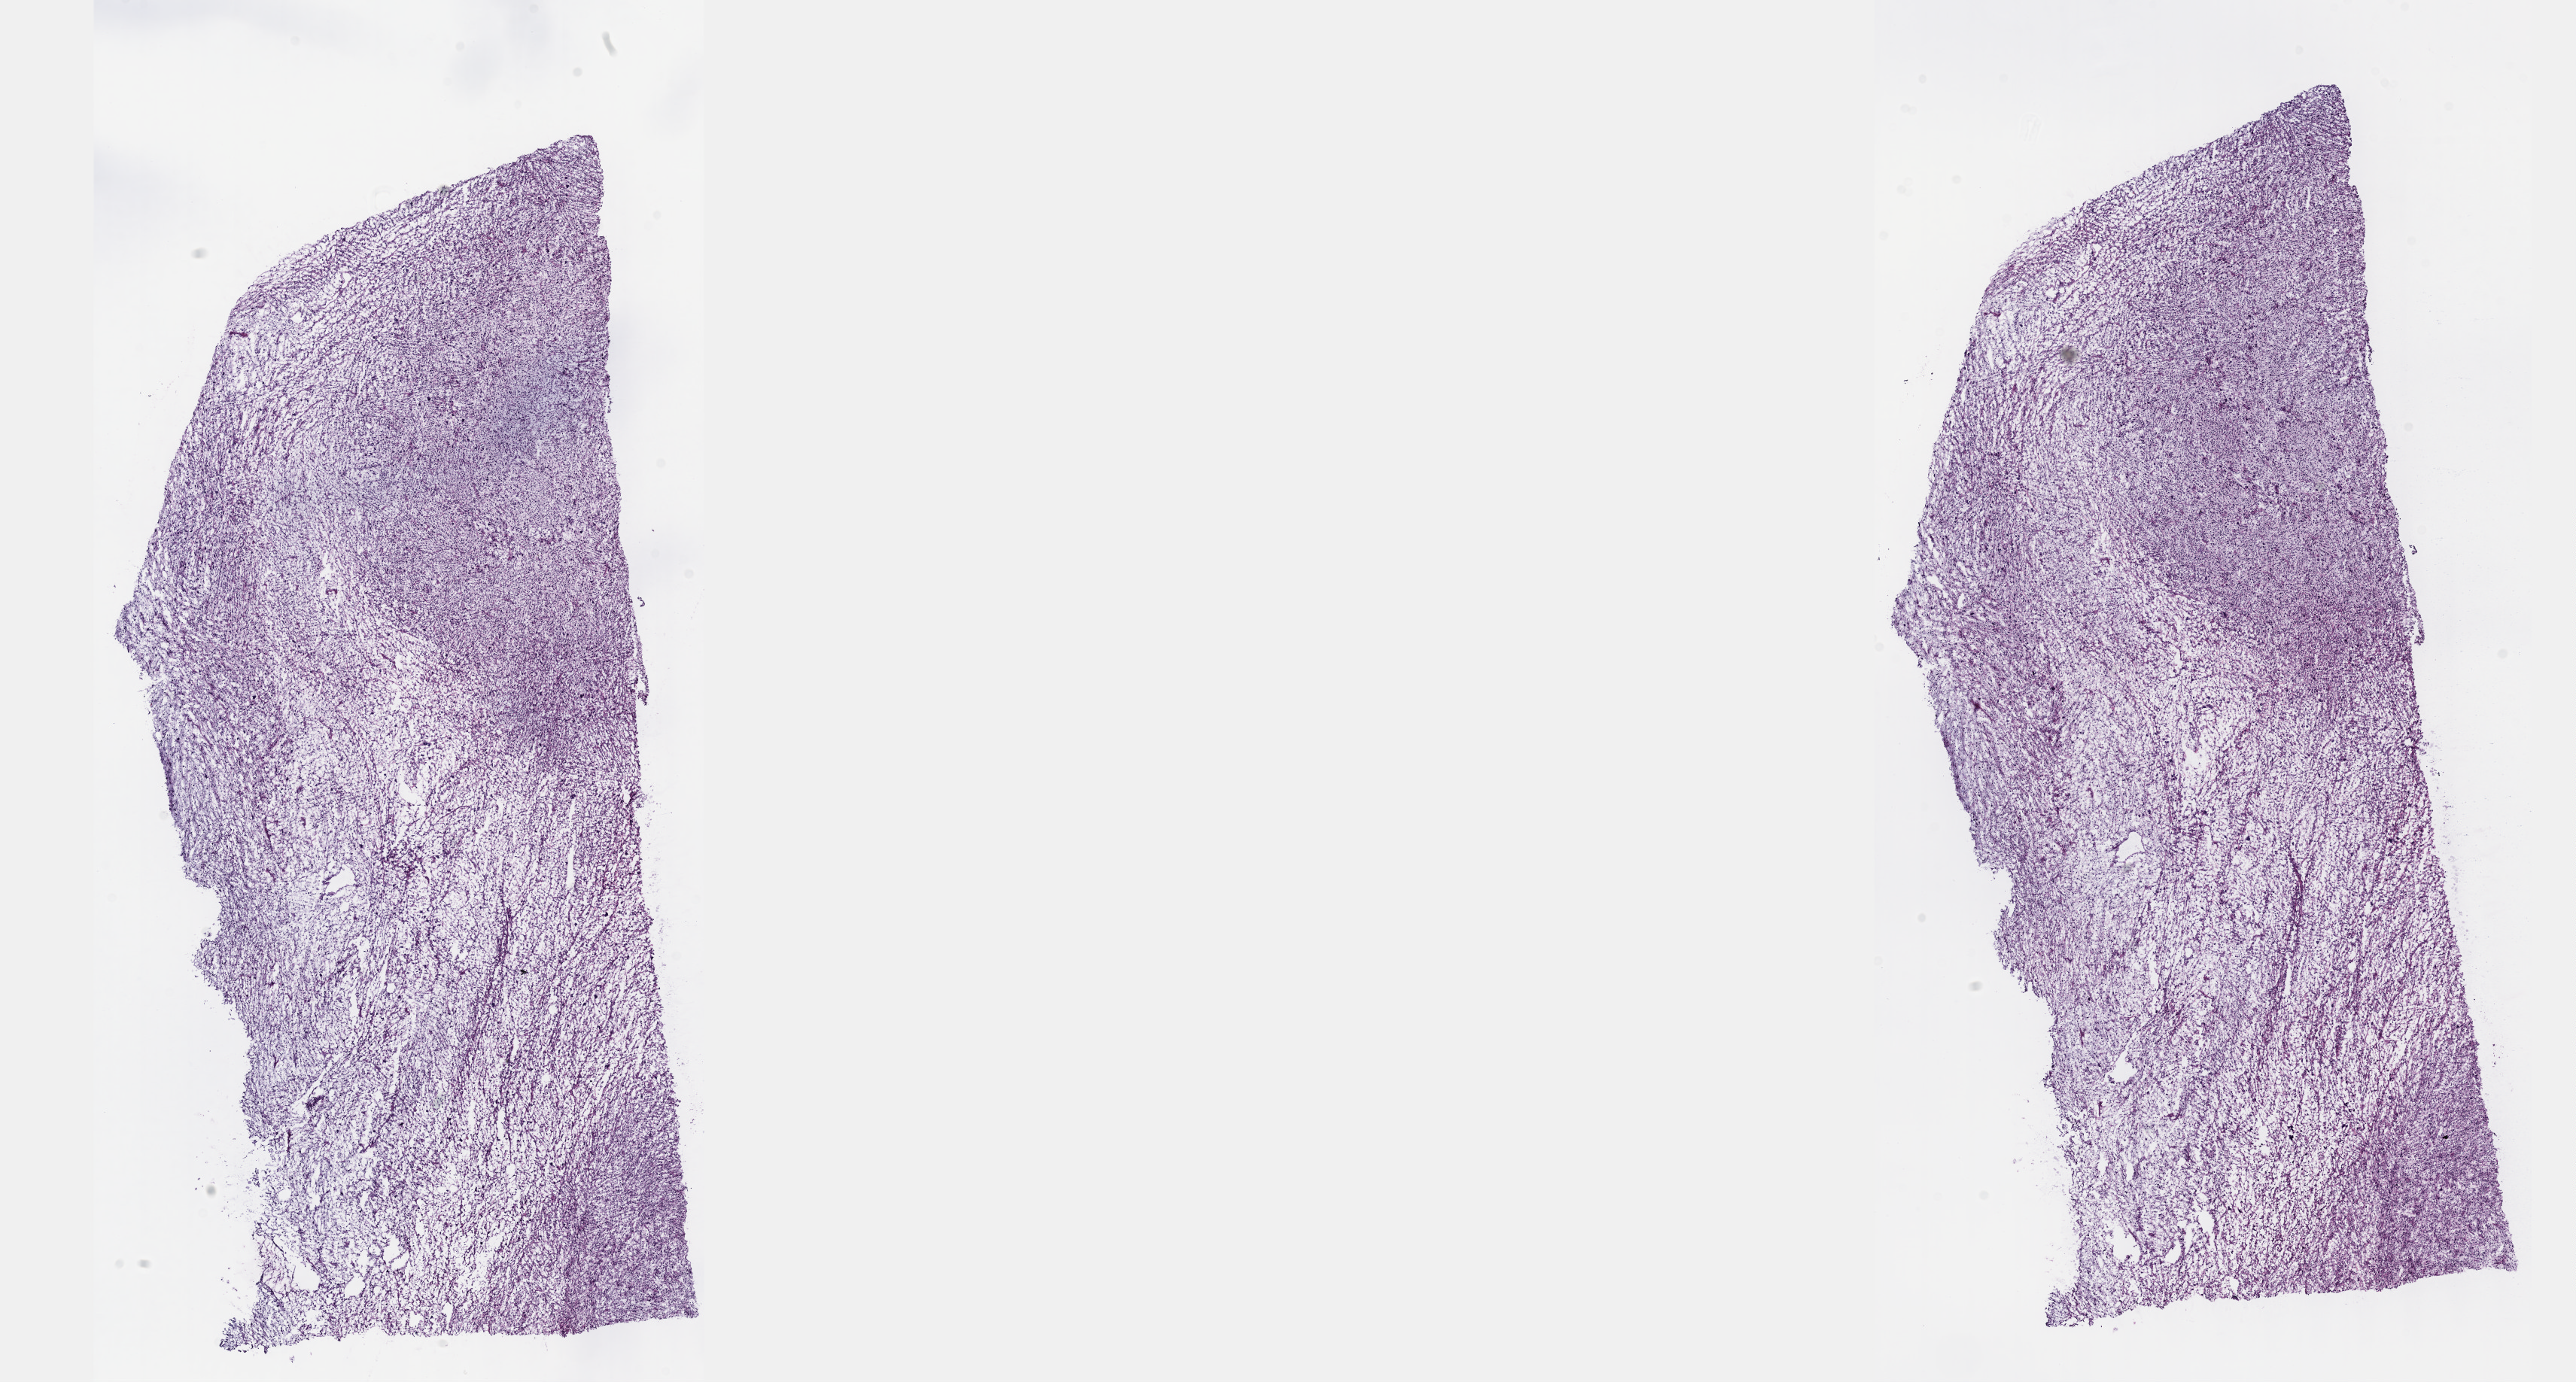
Whole-slide histology image, H&E, shown as a low-resolution overview of the whole scanned area (about 27.7 x 14.8 mm, slide scanned at 40x), frozen section from the top of the tissue portion, connective, subcutaneous and other soft tissues, primary tumour sample. Female, age 72 years at initial diagnosis. Pathologist review of this section (percent, as recorded): tumour cells 60%, tumour nuclei 100%, normal cells 0%, stromal cells 40%, necrosis 0%. Infiltration values recorded for this section: lymphocyte infiltration 0%, monocyte infiltration 0%, neutrophil infiltration 0%.
Pathologic diagnosis: Undifferentiated sarcoma.